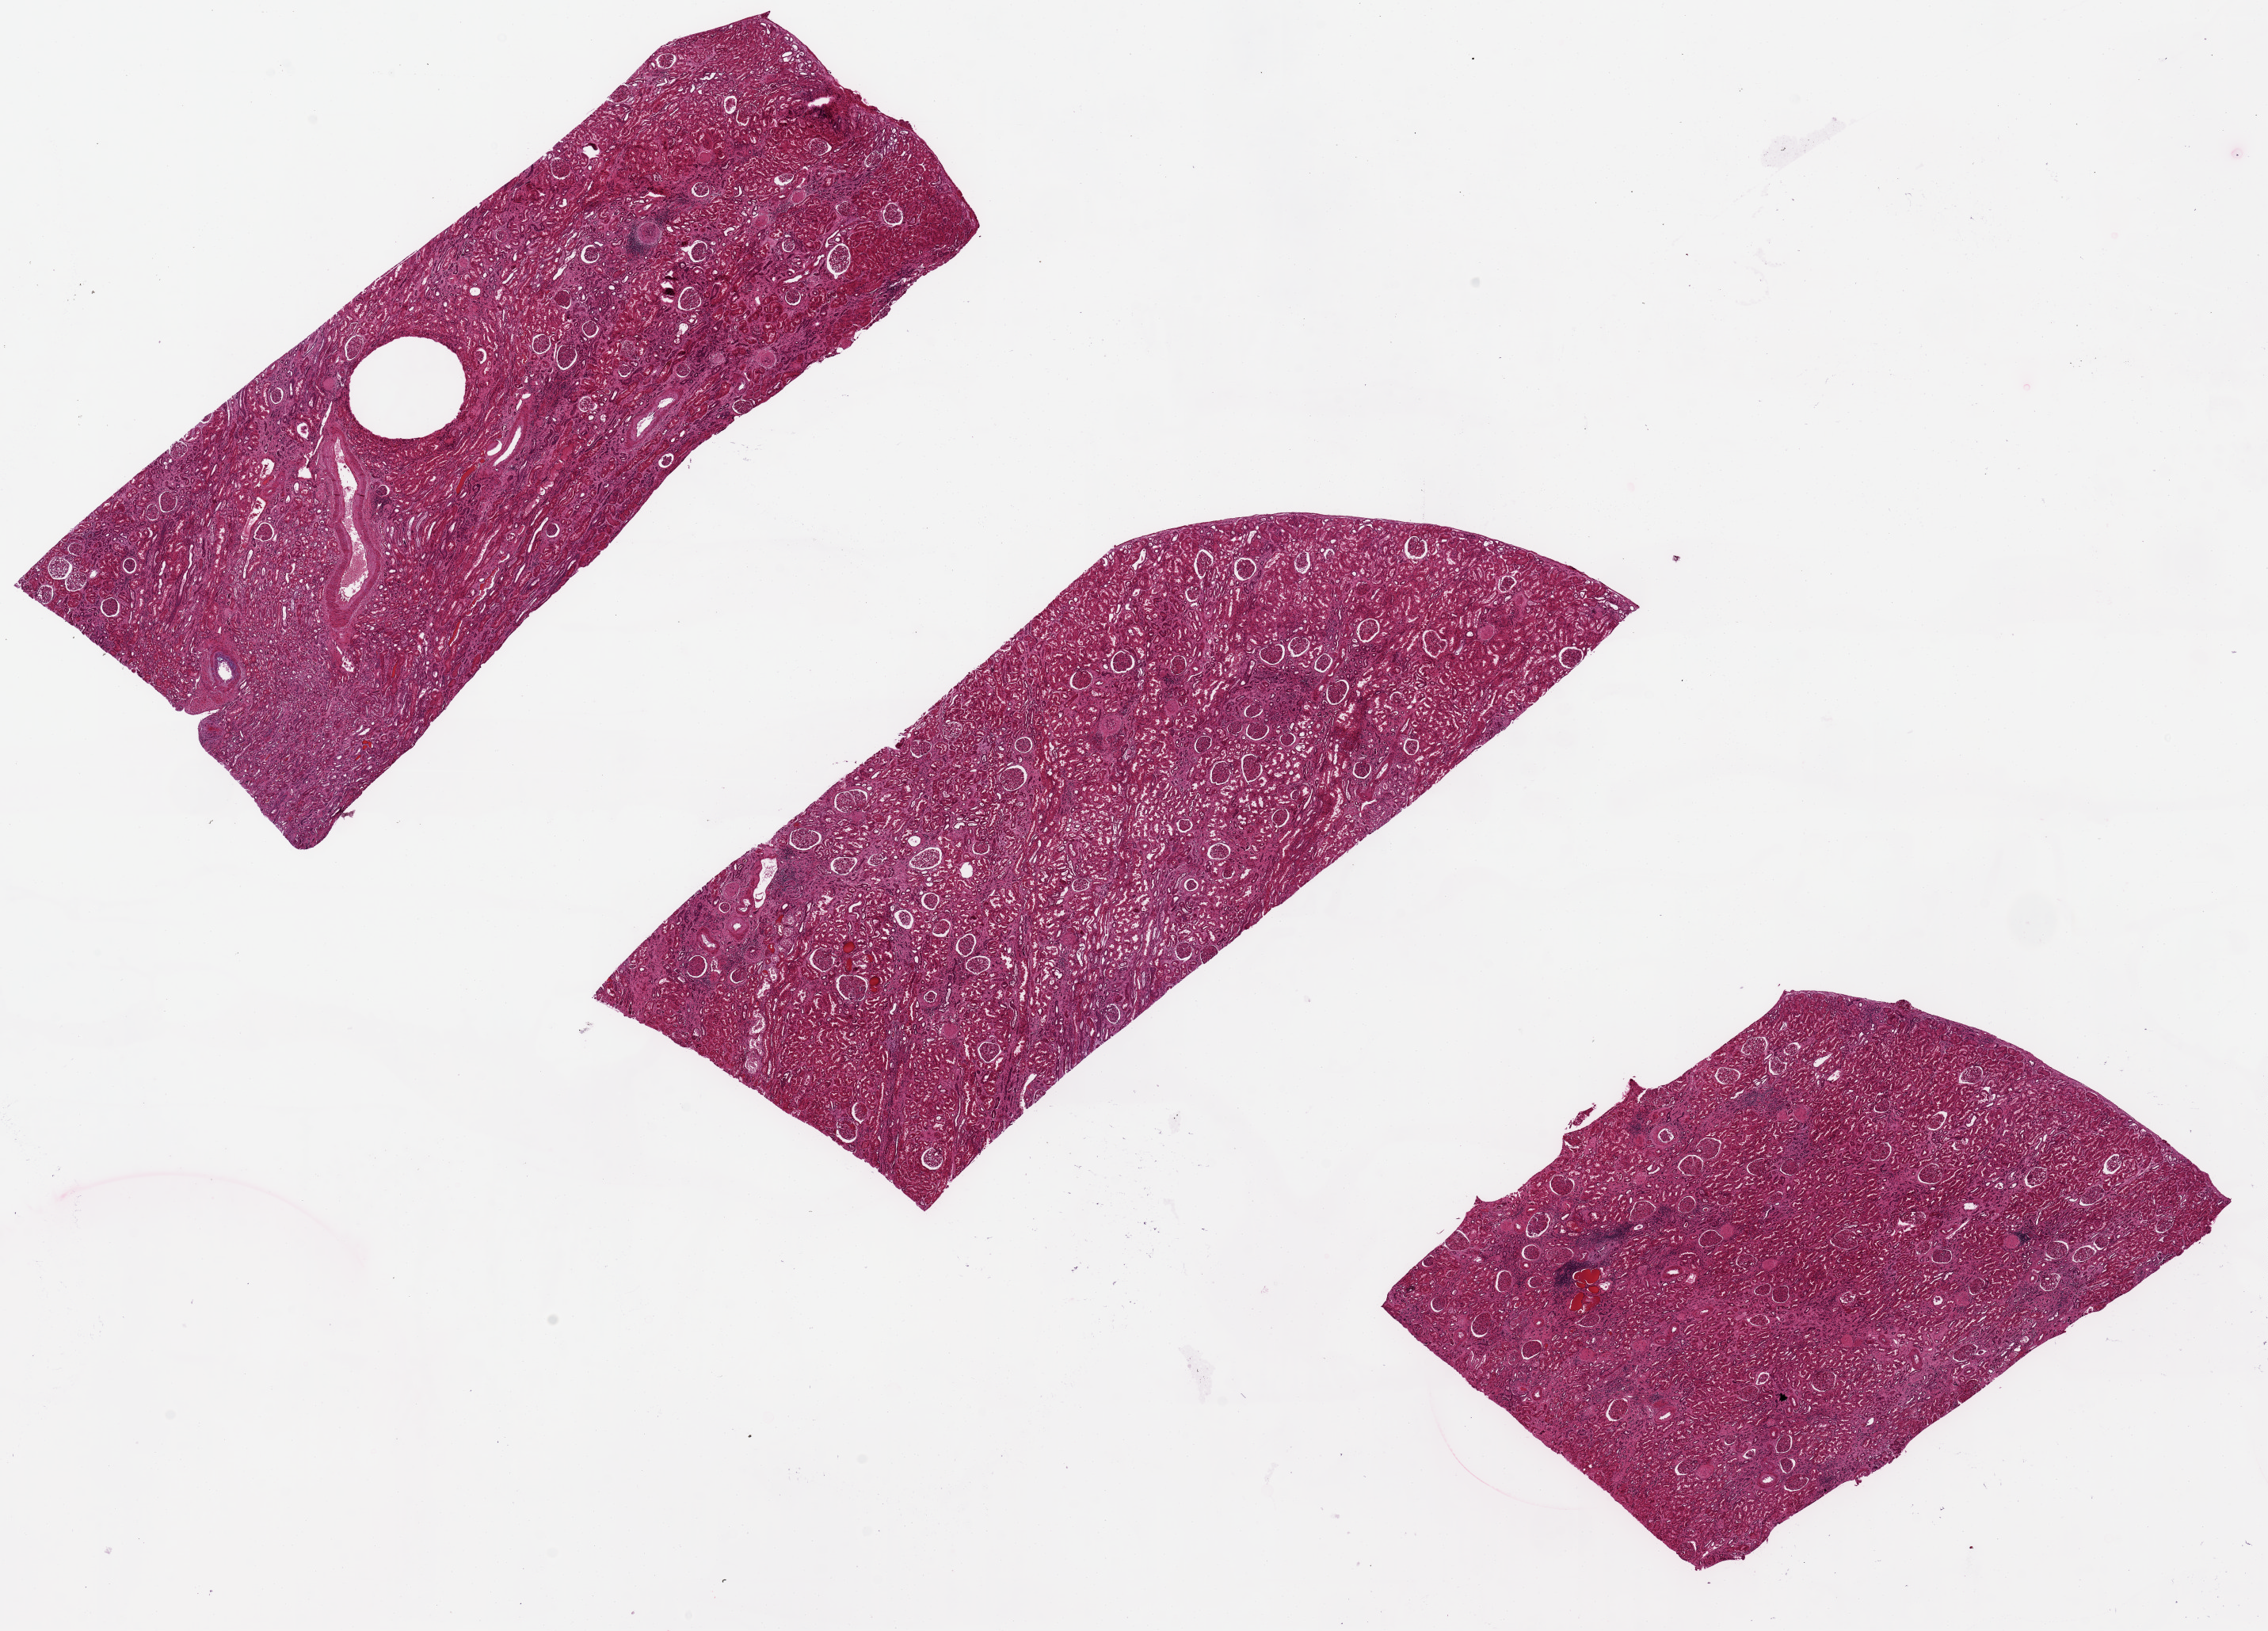
H&E whole-slide image, whole scanned area (about 22.6 x 16.3 mm, from a 20x scan) shown as a low-resolution overview. PAXgene-fixed paraffin-embedded (PFPE) section. Sampled site (target tissue): renal cortex. Donor tissue sample. Donor sex: male.
• reviewer comment on this tissue sample: Patchy interstitial fibrosing nephritis, moderate; arterial and arteriolar nephrosclerosis (vascular and glomerular sclerosis) (See Attachment A)